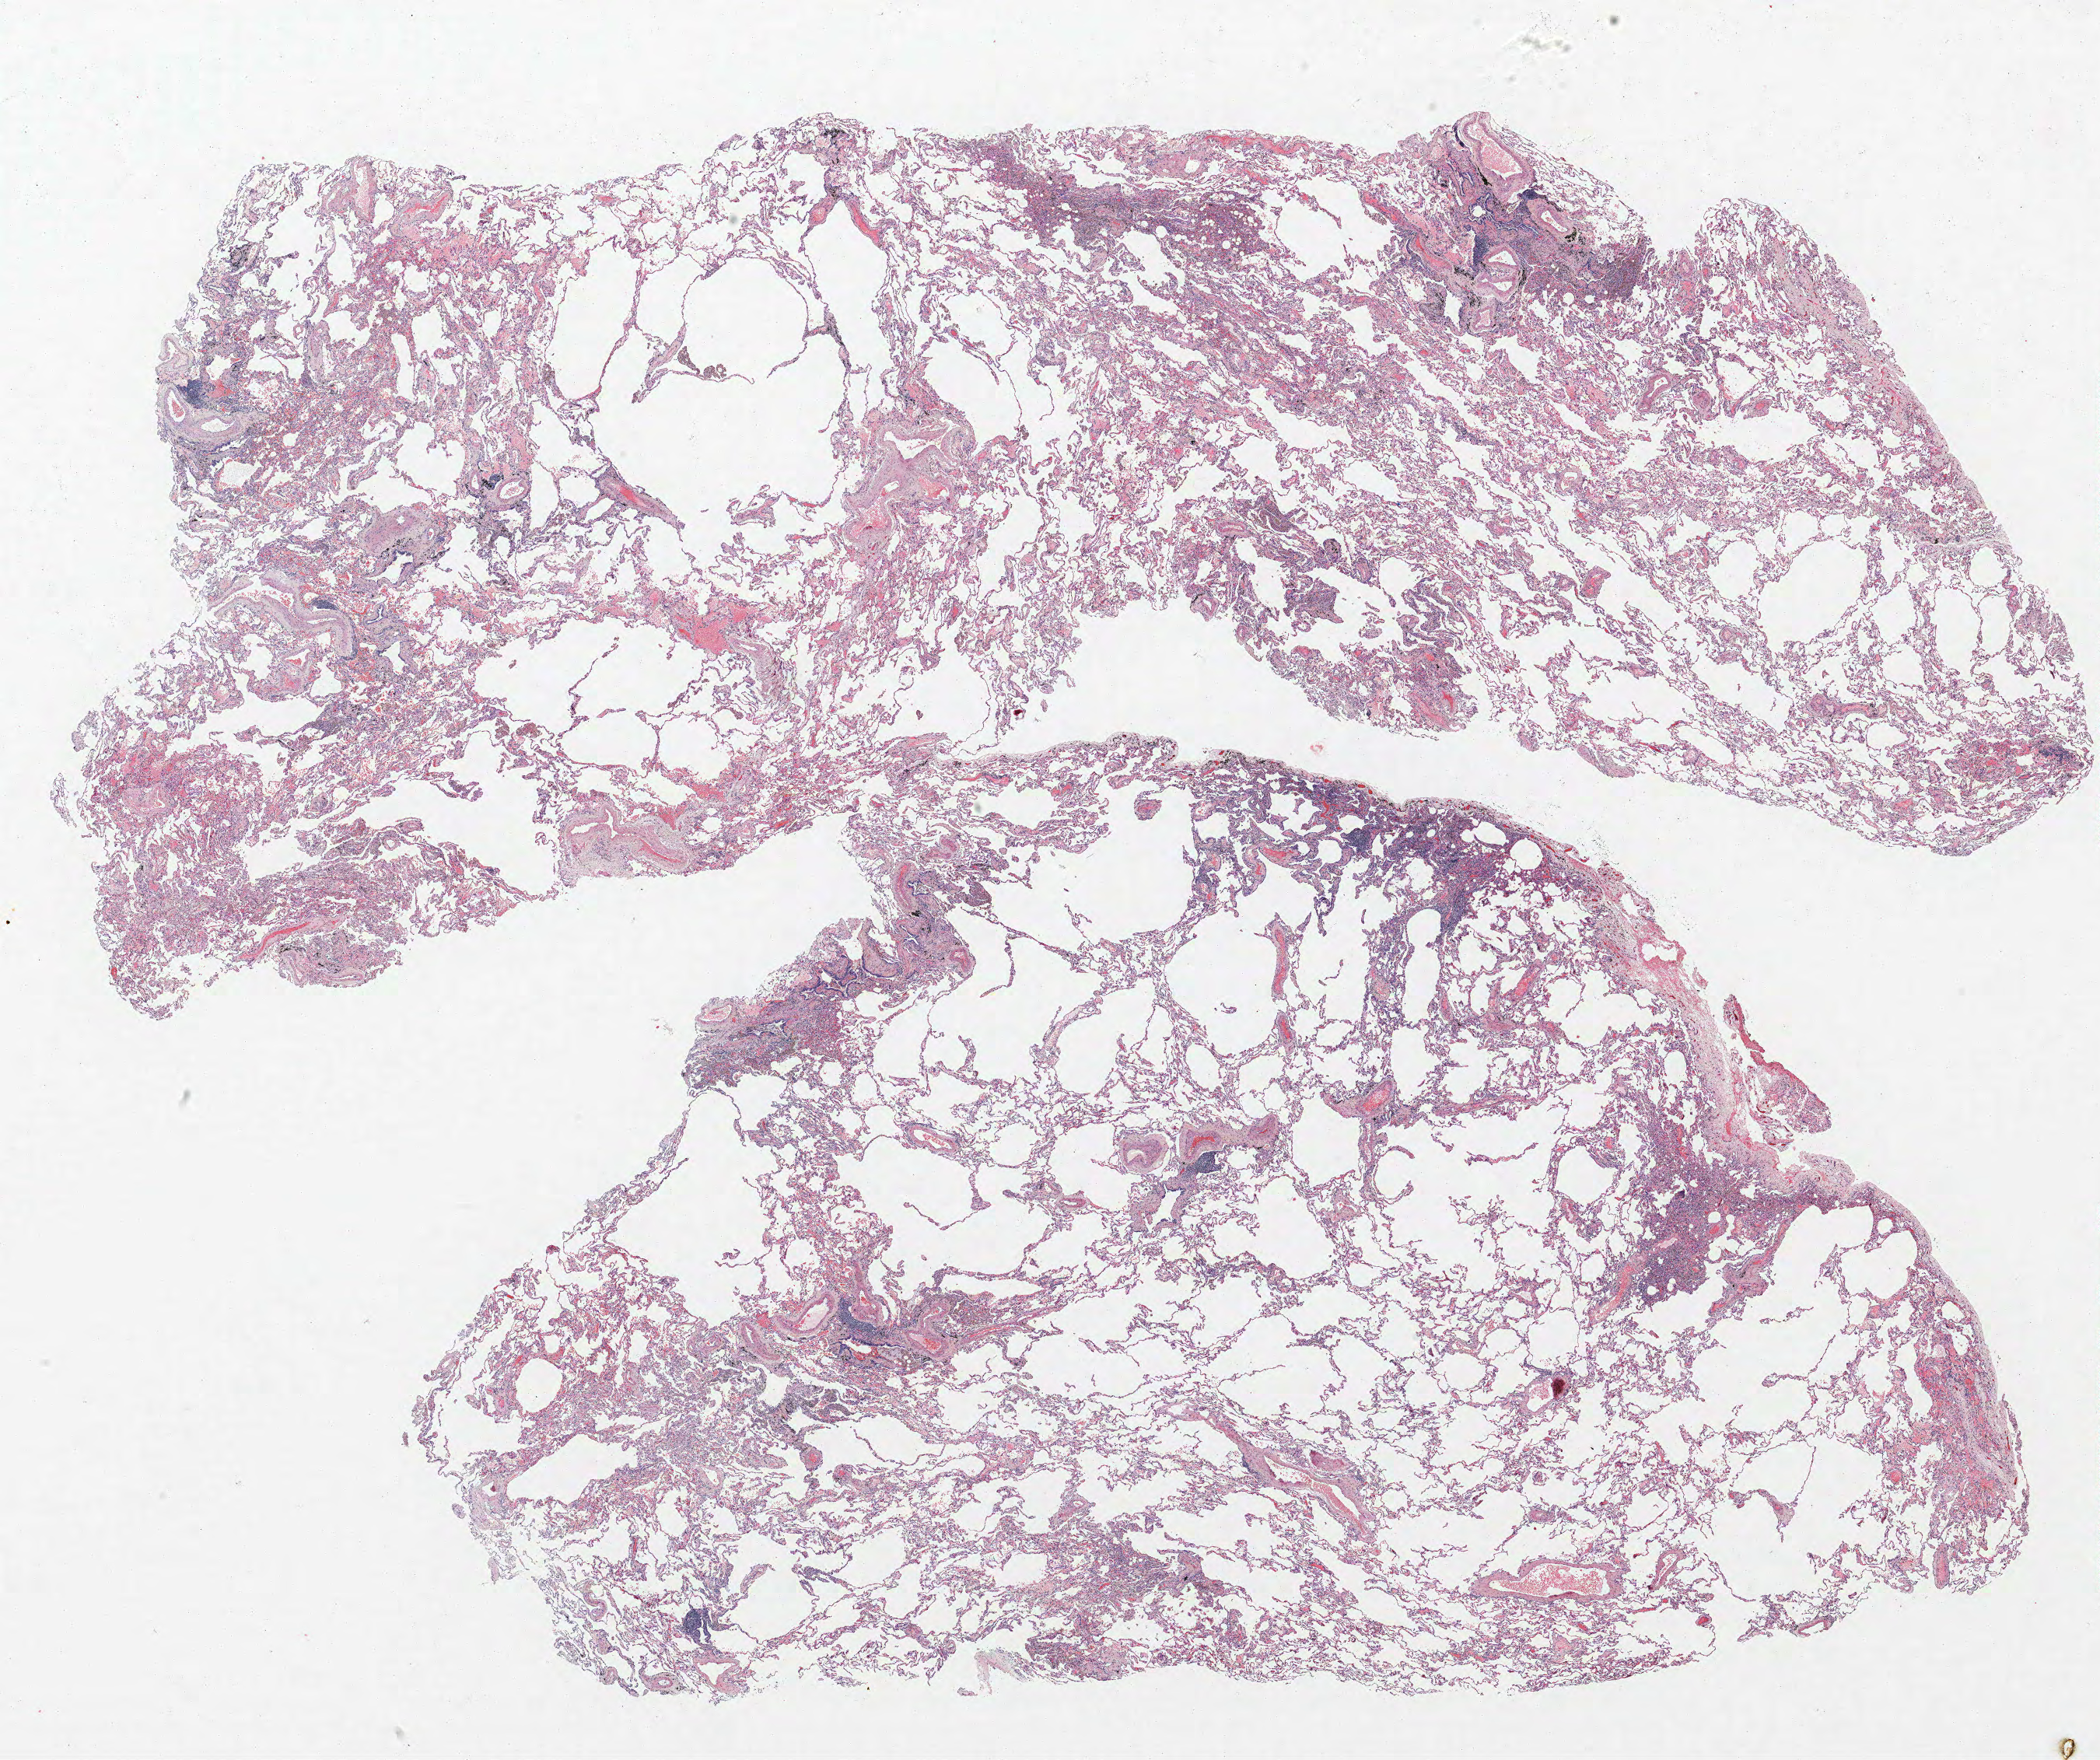
Whole-slide histology image, H&E-stained — a low-resolution overview of the entire scanned area, about 21.6 x 18.1 mm (acquisition: 40x scan); formalin-fixed paraffin-embedded (FFPE) section; lung tissue. Female patient, aged 64 at enrolment. Current smoker at enrolment.
Participant's lung-cancer diagnosis: Adenocarcinoma, NOS.